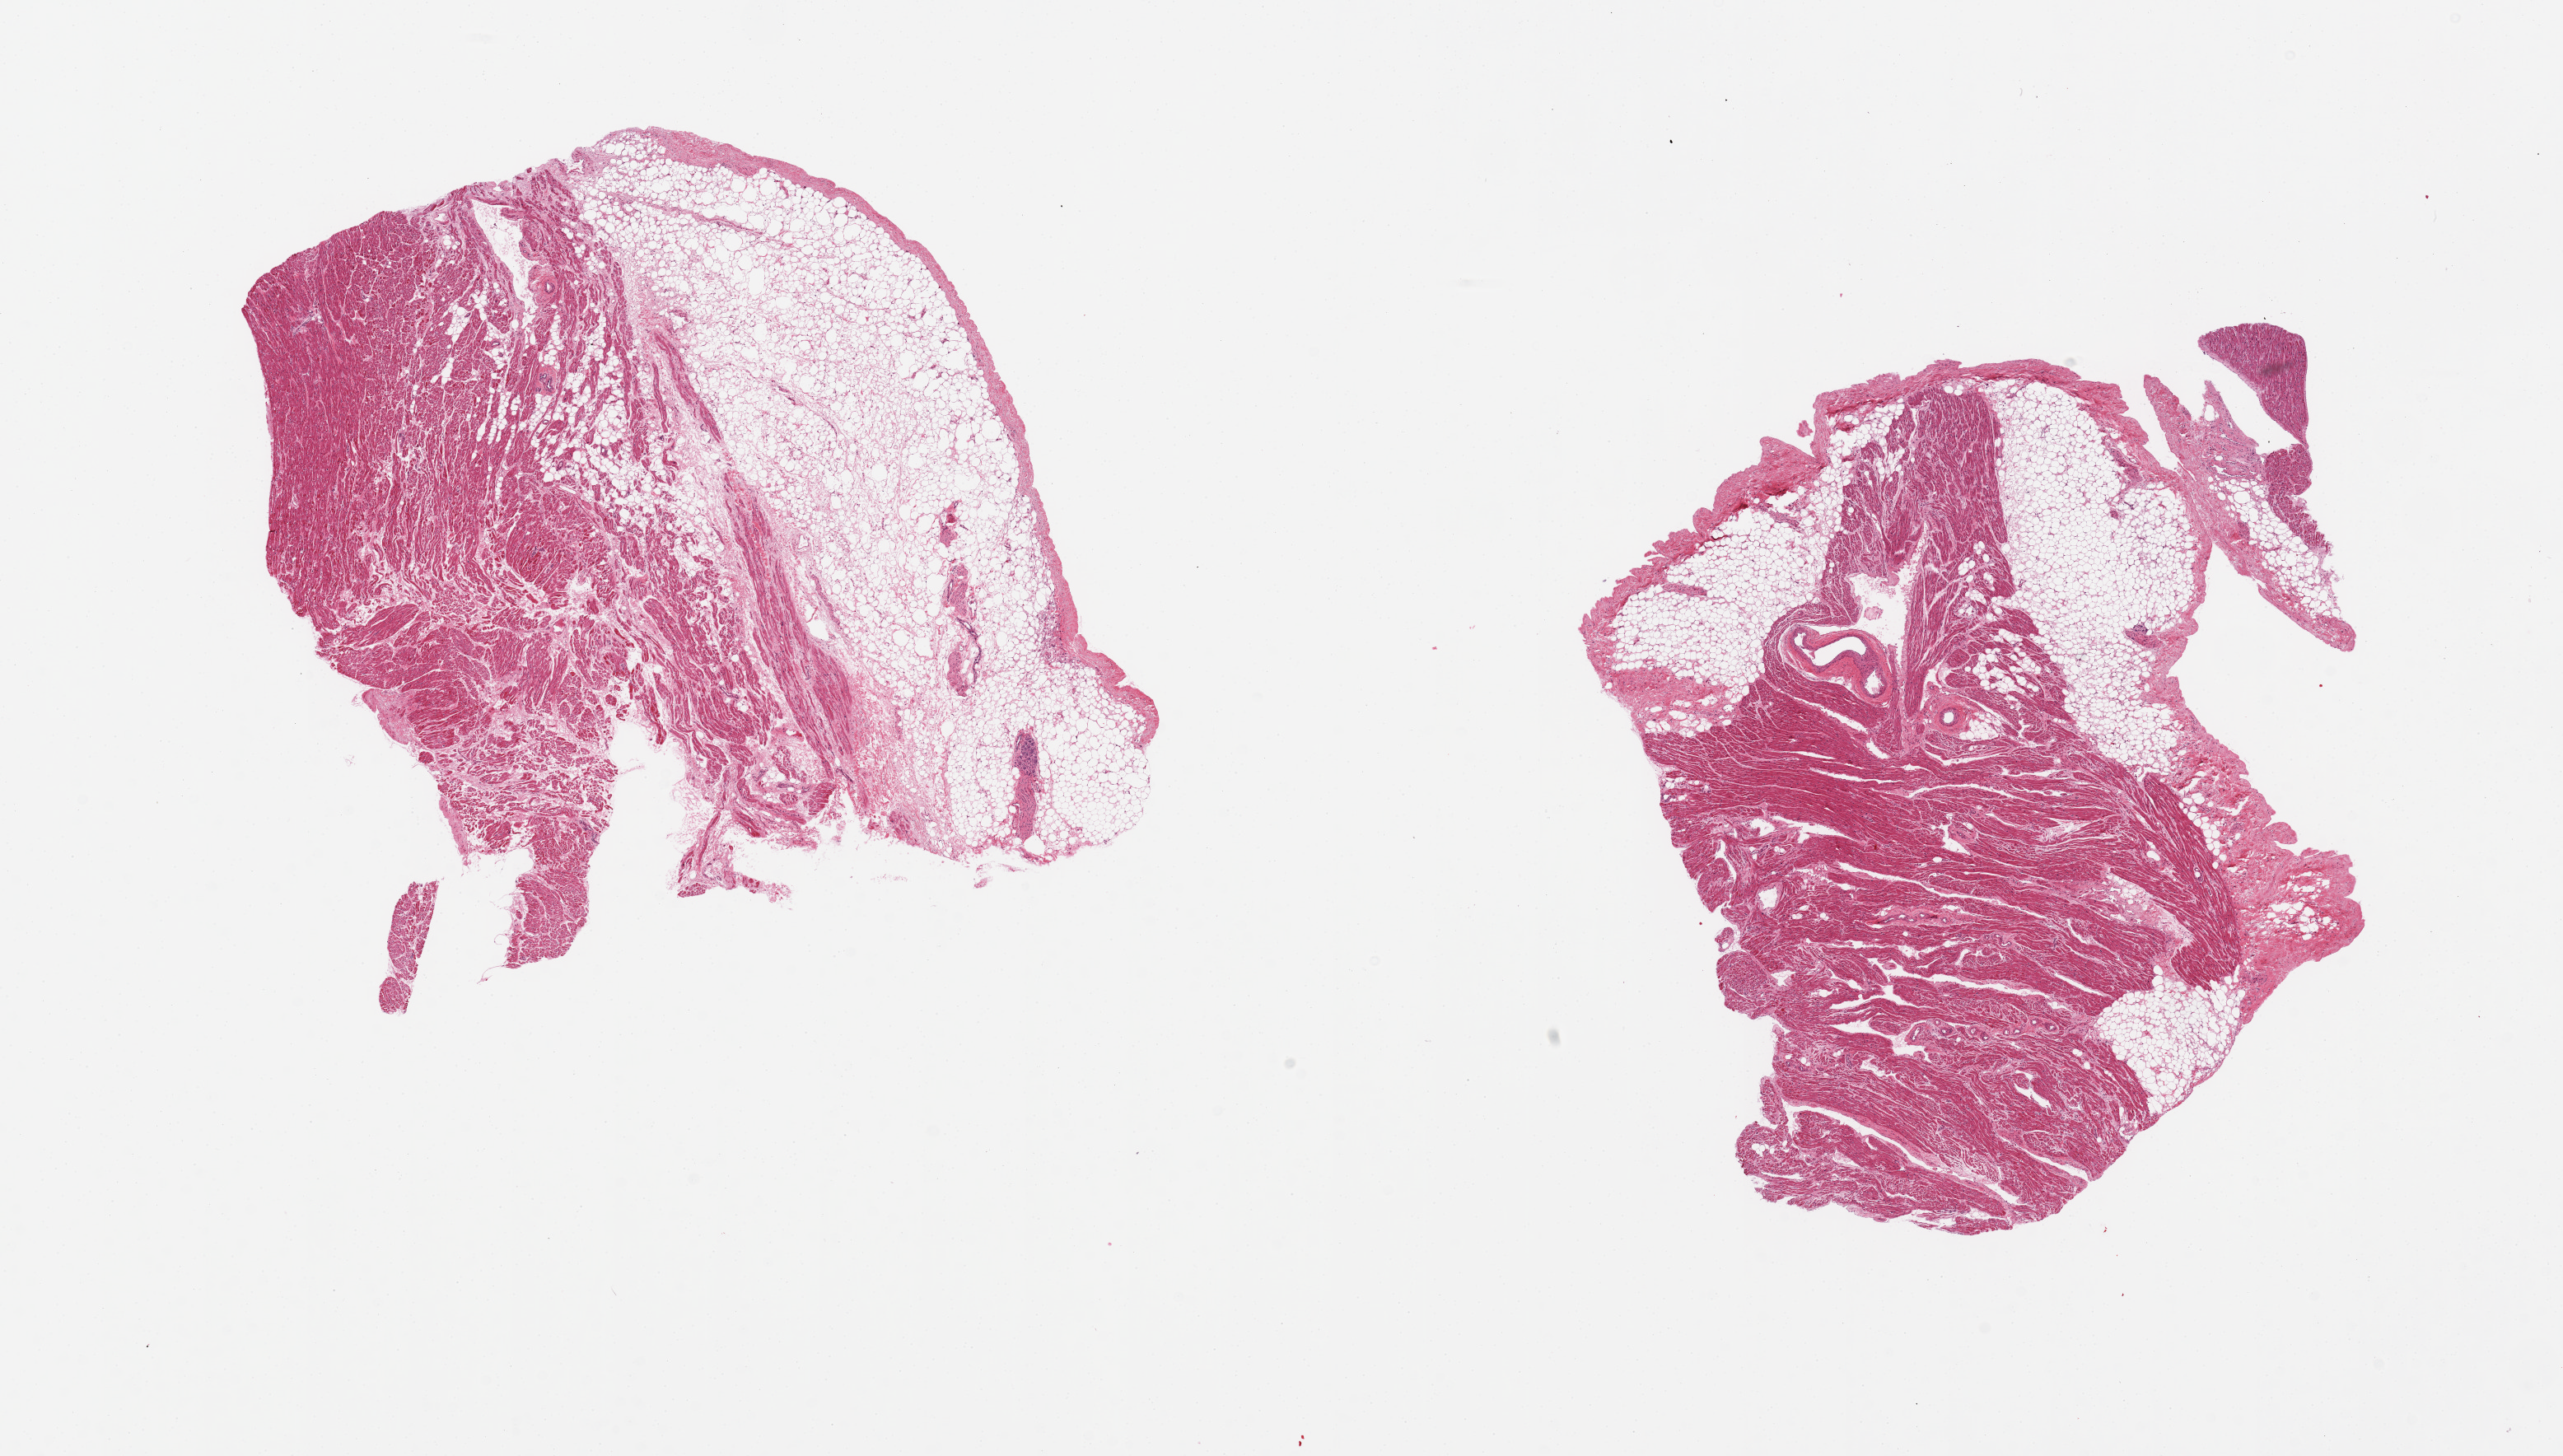
Hematoxylin and eosin (H&E) whole-slide image — low-resolution overview of the scanned area, about 24.6 x 14.0 mm. PAXgene-fixed, paraffin-embedded tissue. Target tissue: auricular appendage. Donor tissue sample. Donor sex: female.
Reviewer comment on this tissue sample: 2 pieces, 30-50% fat, interstitial fibrosis.